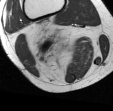
MRI of an extremity soft-tissue mass, one axial slice. Slice 36 of 45 in the series (ordered by position). MR volume resampled by the dataset authors to the PET/CT grid (not the native acquisition matrix). 3.27 mm slice thickness. 113 × 111 image matrix, field of view 110 × 108 mm. Female patient. Case-level facts recorded for this patient, not image findings: histological type: liposarcoma; site of the primary tumour: right thigh.
Structures marked on this image (expert contour drawn on MRI and transferred to this co-registered scan by the dataset authors):
- gross tumour volume (mass): bounding box <51,40,77,54> (left, top, right, bottom; pixels)